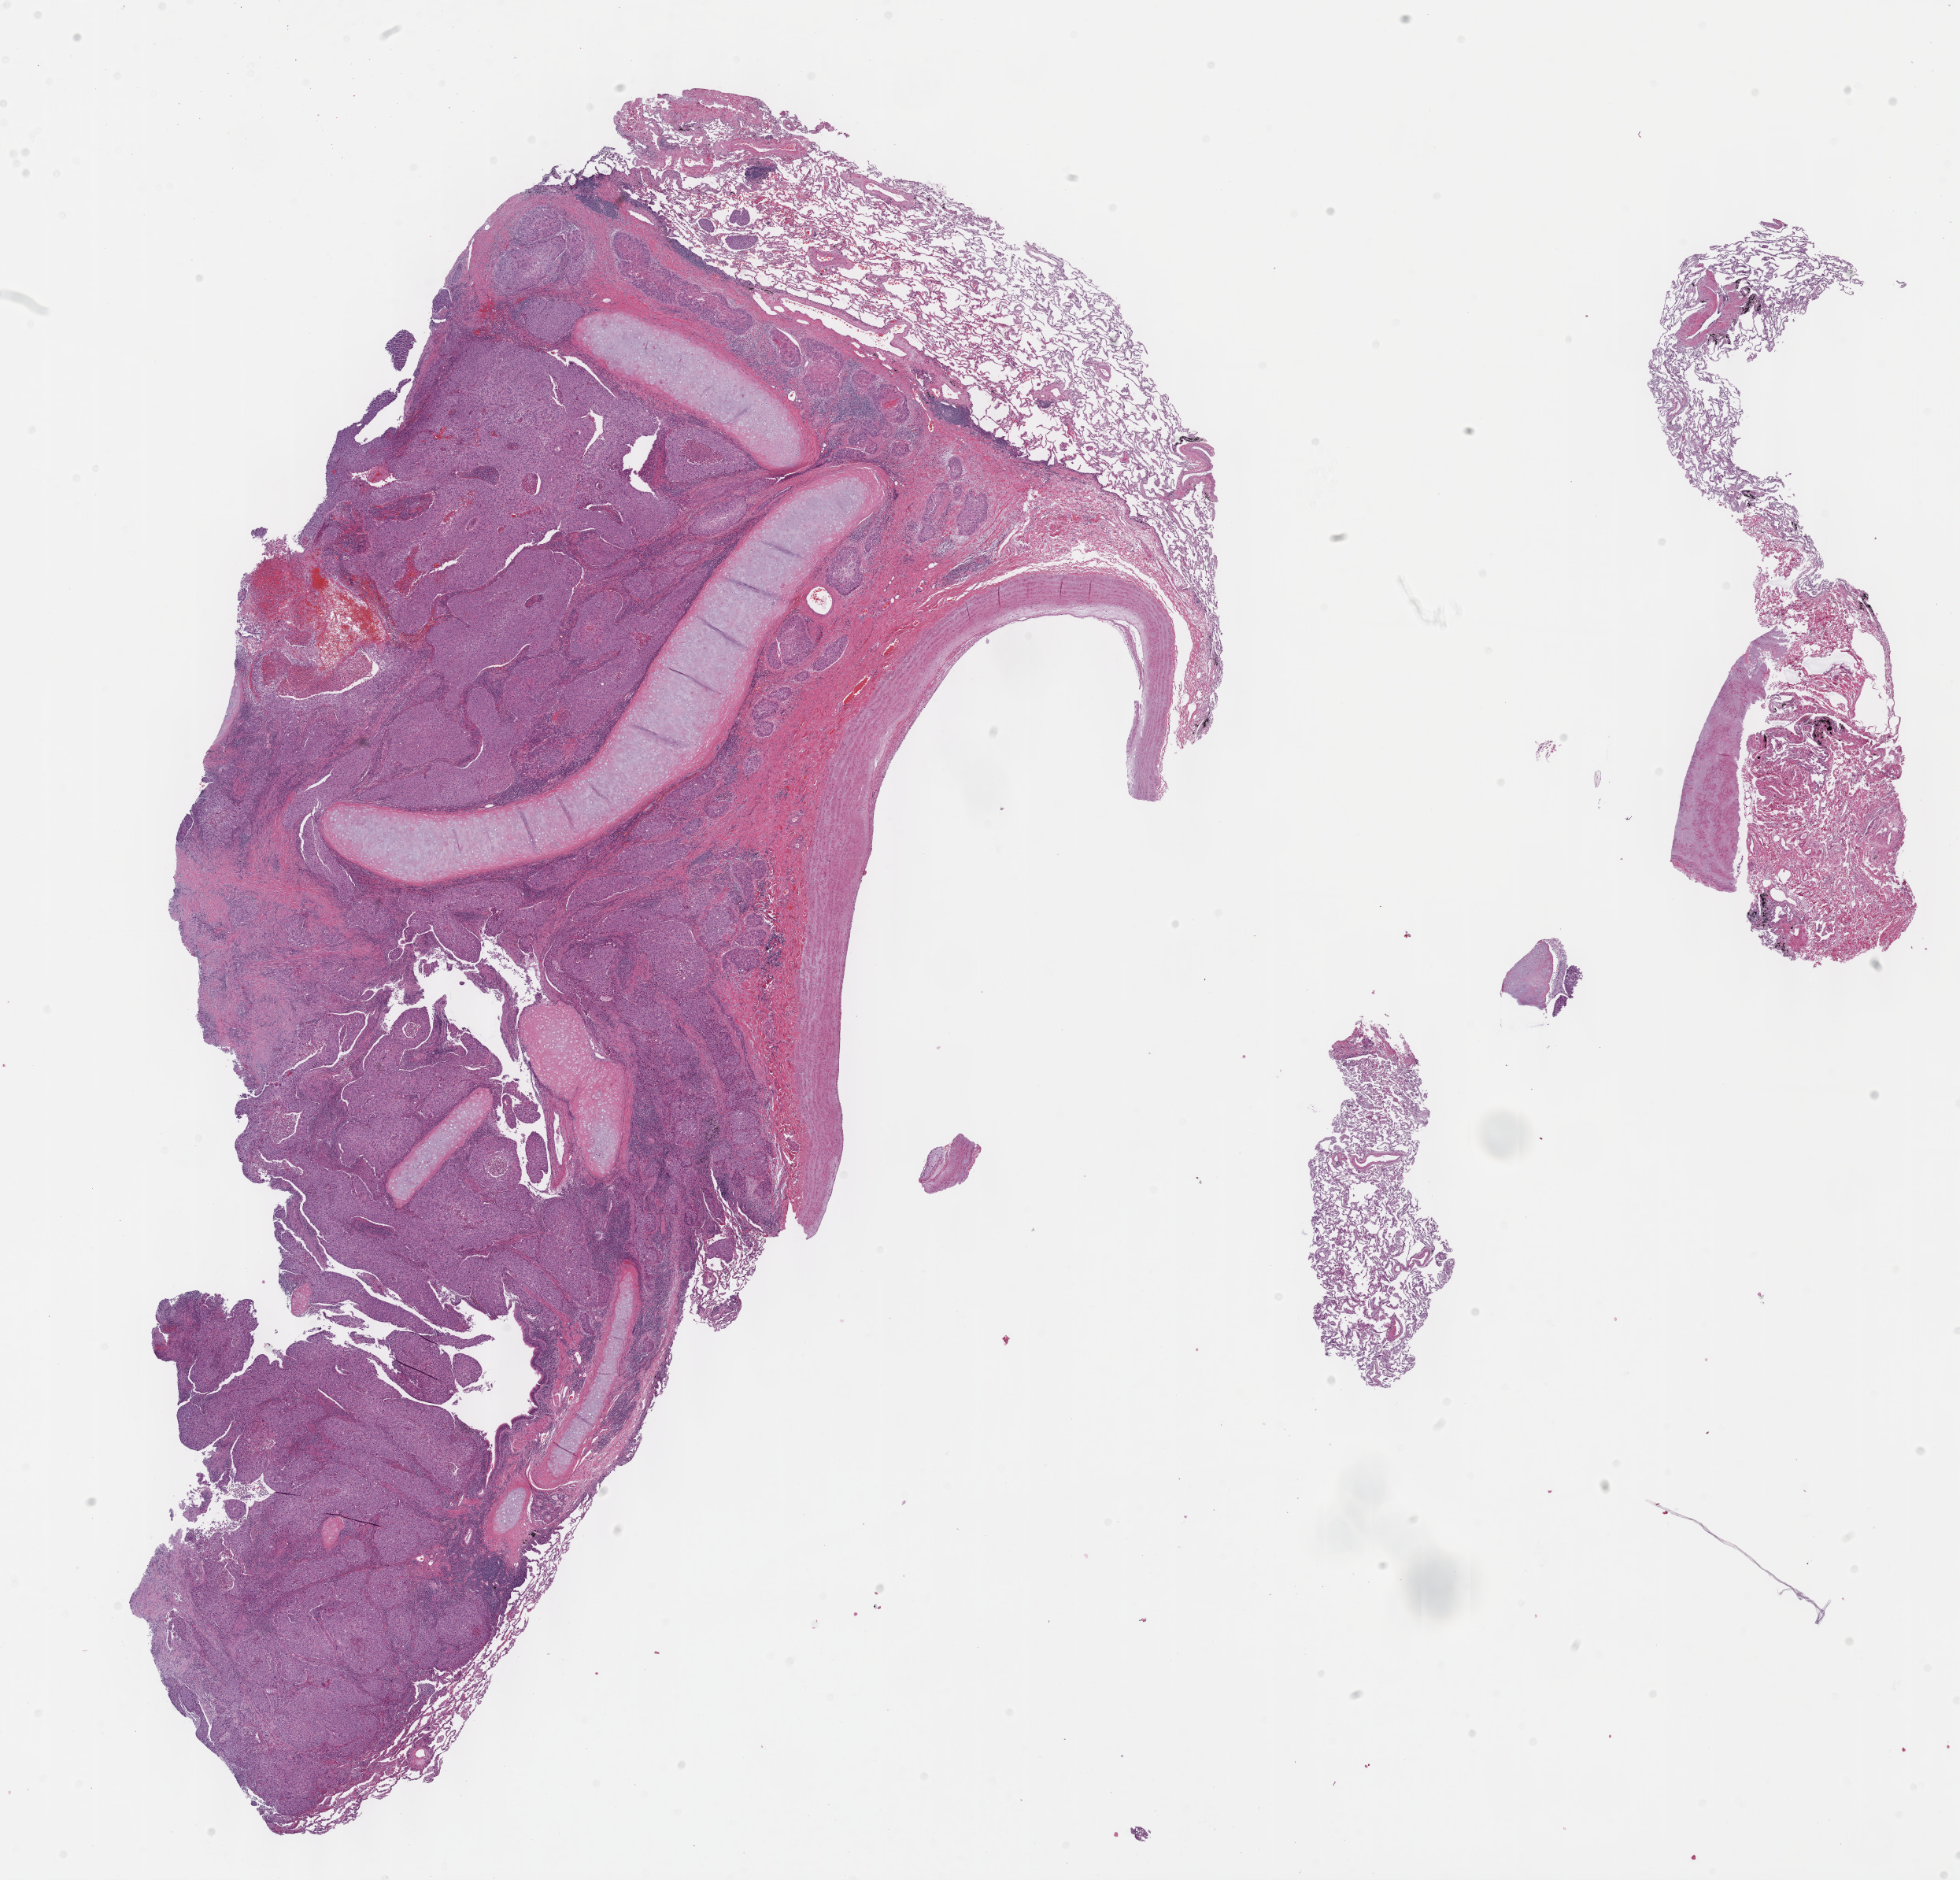
H&E-stained whole-slide image — low-resolution overview of the scanned area, about 20.1 x 19.3 mm. Formalin-fixed paraffin-embedded (FFPE) diagnostic section. Sample: primary tumour, lung. Patient: male, age at initial diagnosis 71 years.
AJCC pathologic stage: IIA. Pathologic diagnosis: Squamous cell carcinoma, NOS.